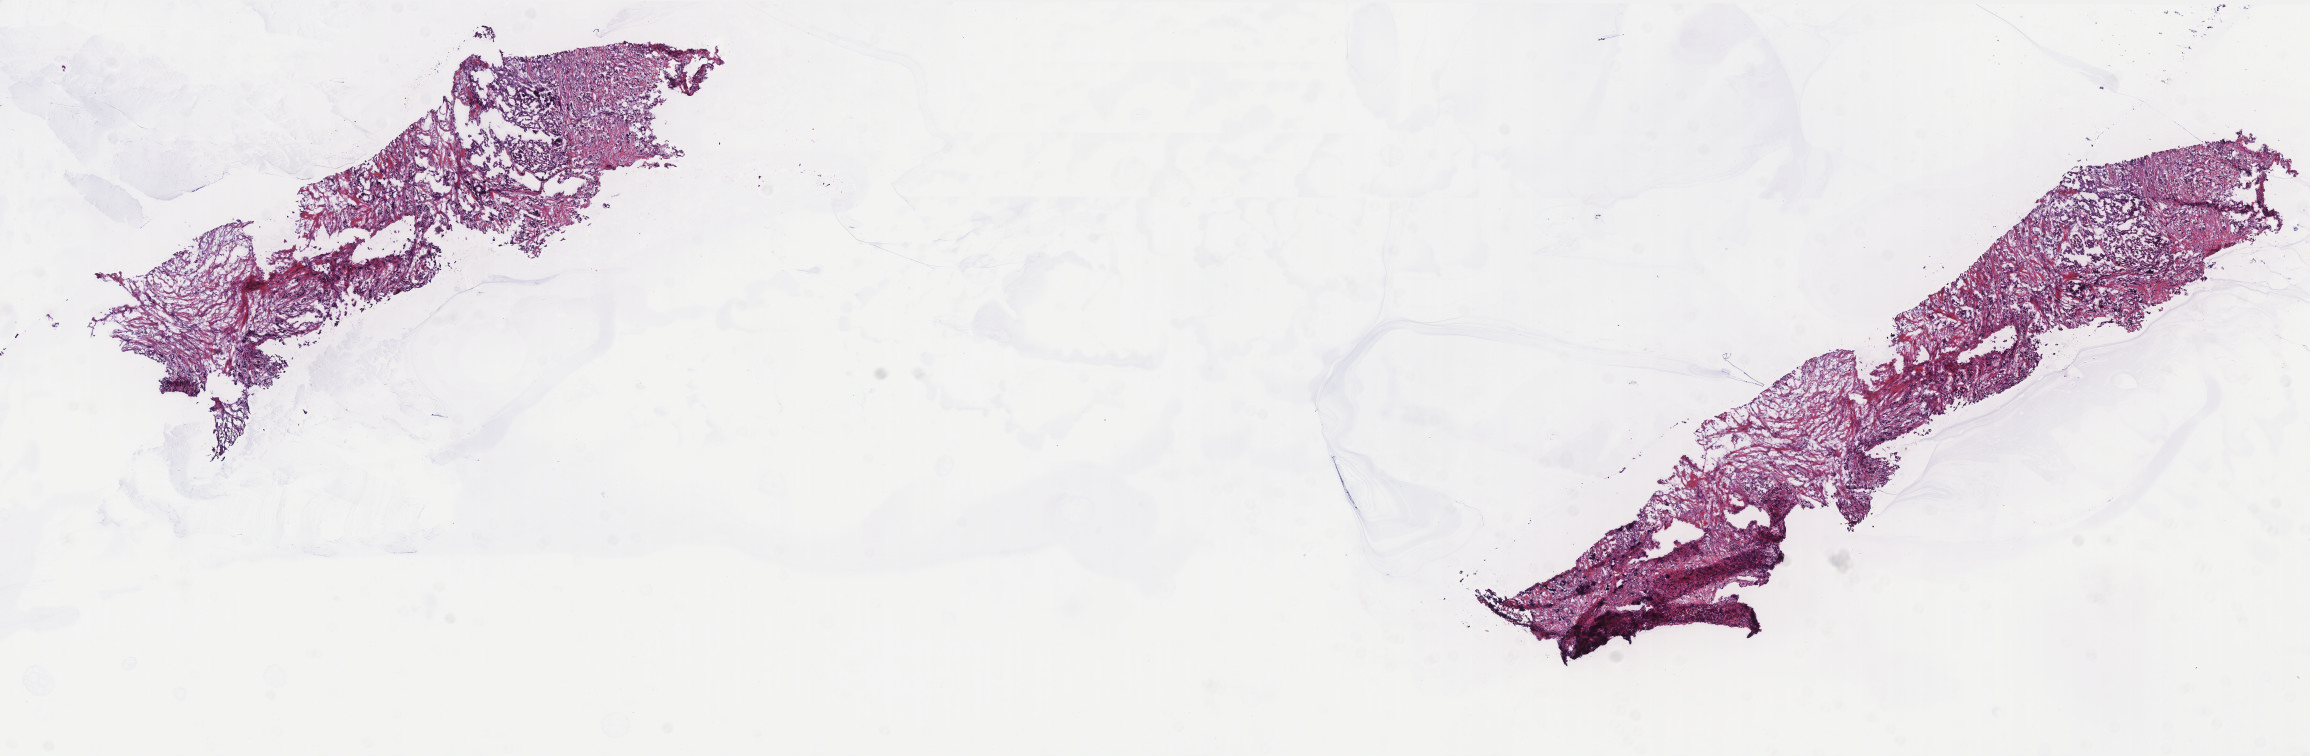
Whole-slide histology image, H&E-stained — shown as a low-resolution overview of the whole scanned area (about 18.5 x 6.1 mm, slide scanned at 40x). Frozen section. Primary tumour sample from the breast. Female patient; age at initial diagnosis 74 years. Slide review estimates, as recorded: tumour cells 80%, tumour nuclei 85%, normal cells 0%, stromal cells 19%, necrosis 1%. Inflammatory infiltration, as recorded: lymphocyte infiltration 3%, monocyte infiltration 0%, neutrophil infiltration 0%.
AJCC pathologic stage: IIA. Histologic diagnosis: Infiltrating duct carcinoma, NOS. Lymph nodes positive (case pathology): 0 of 19 examined.